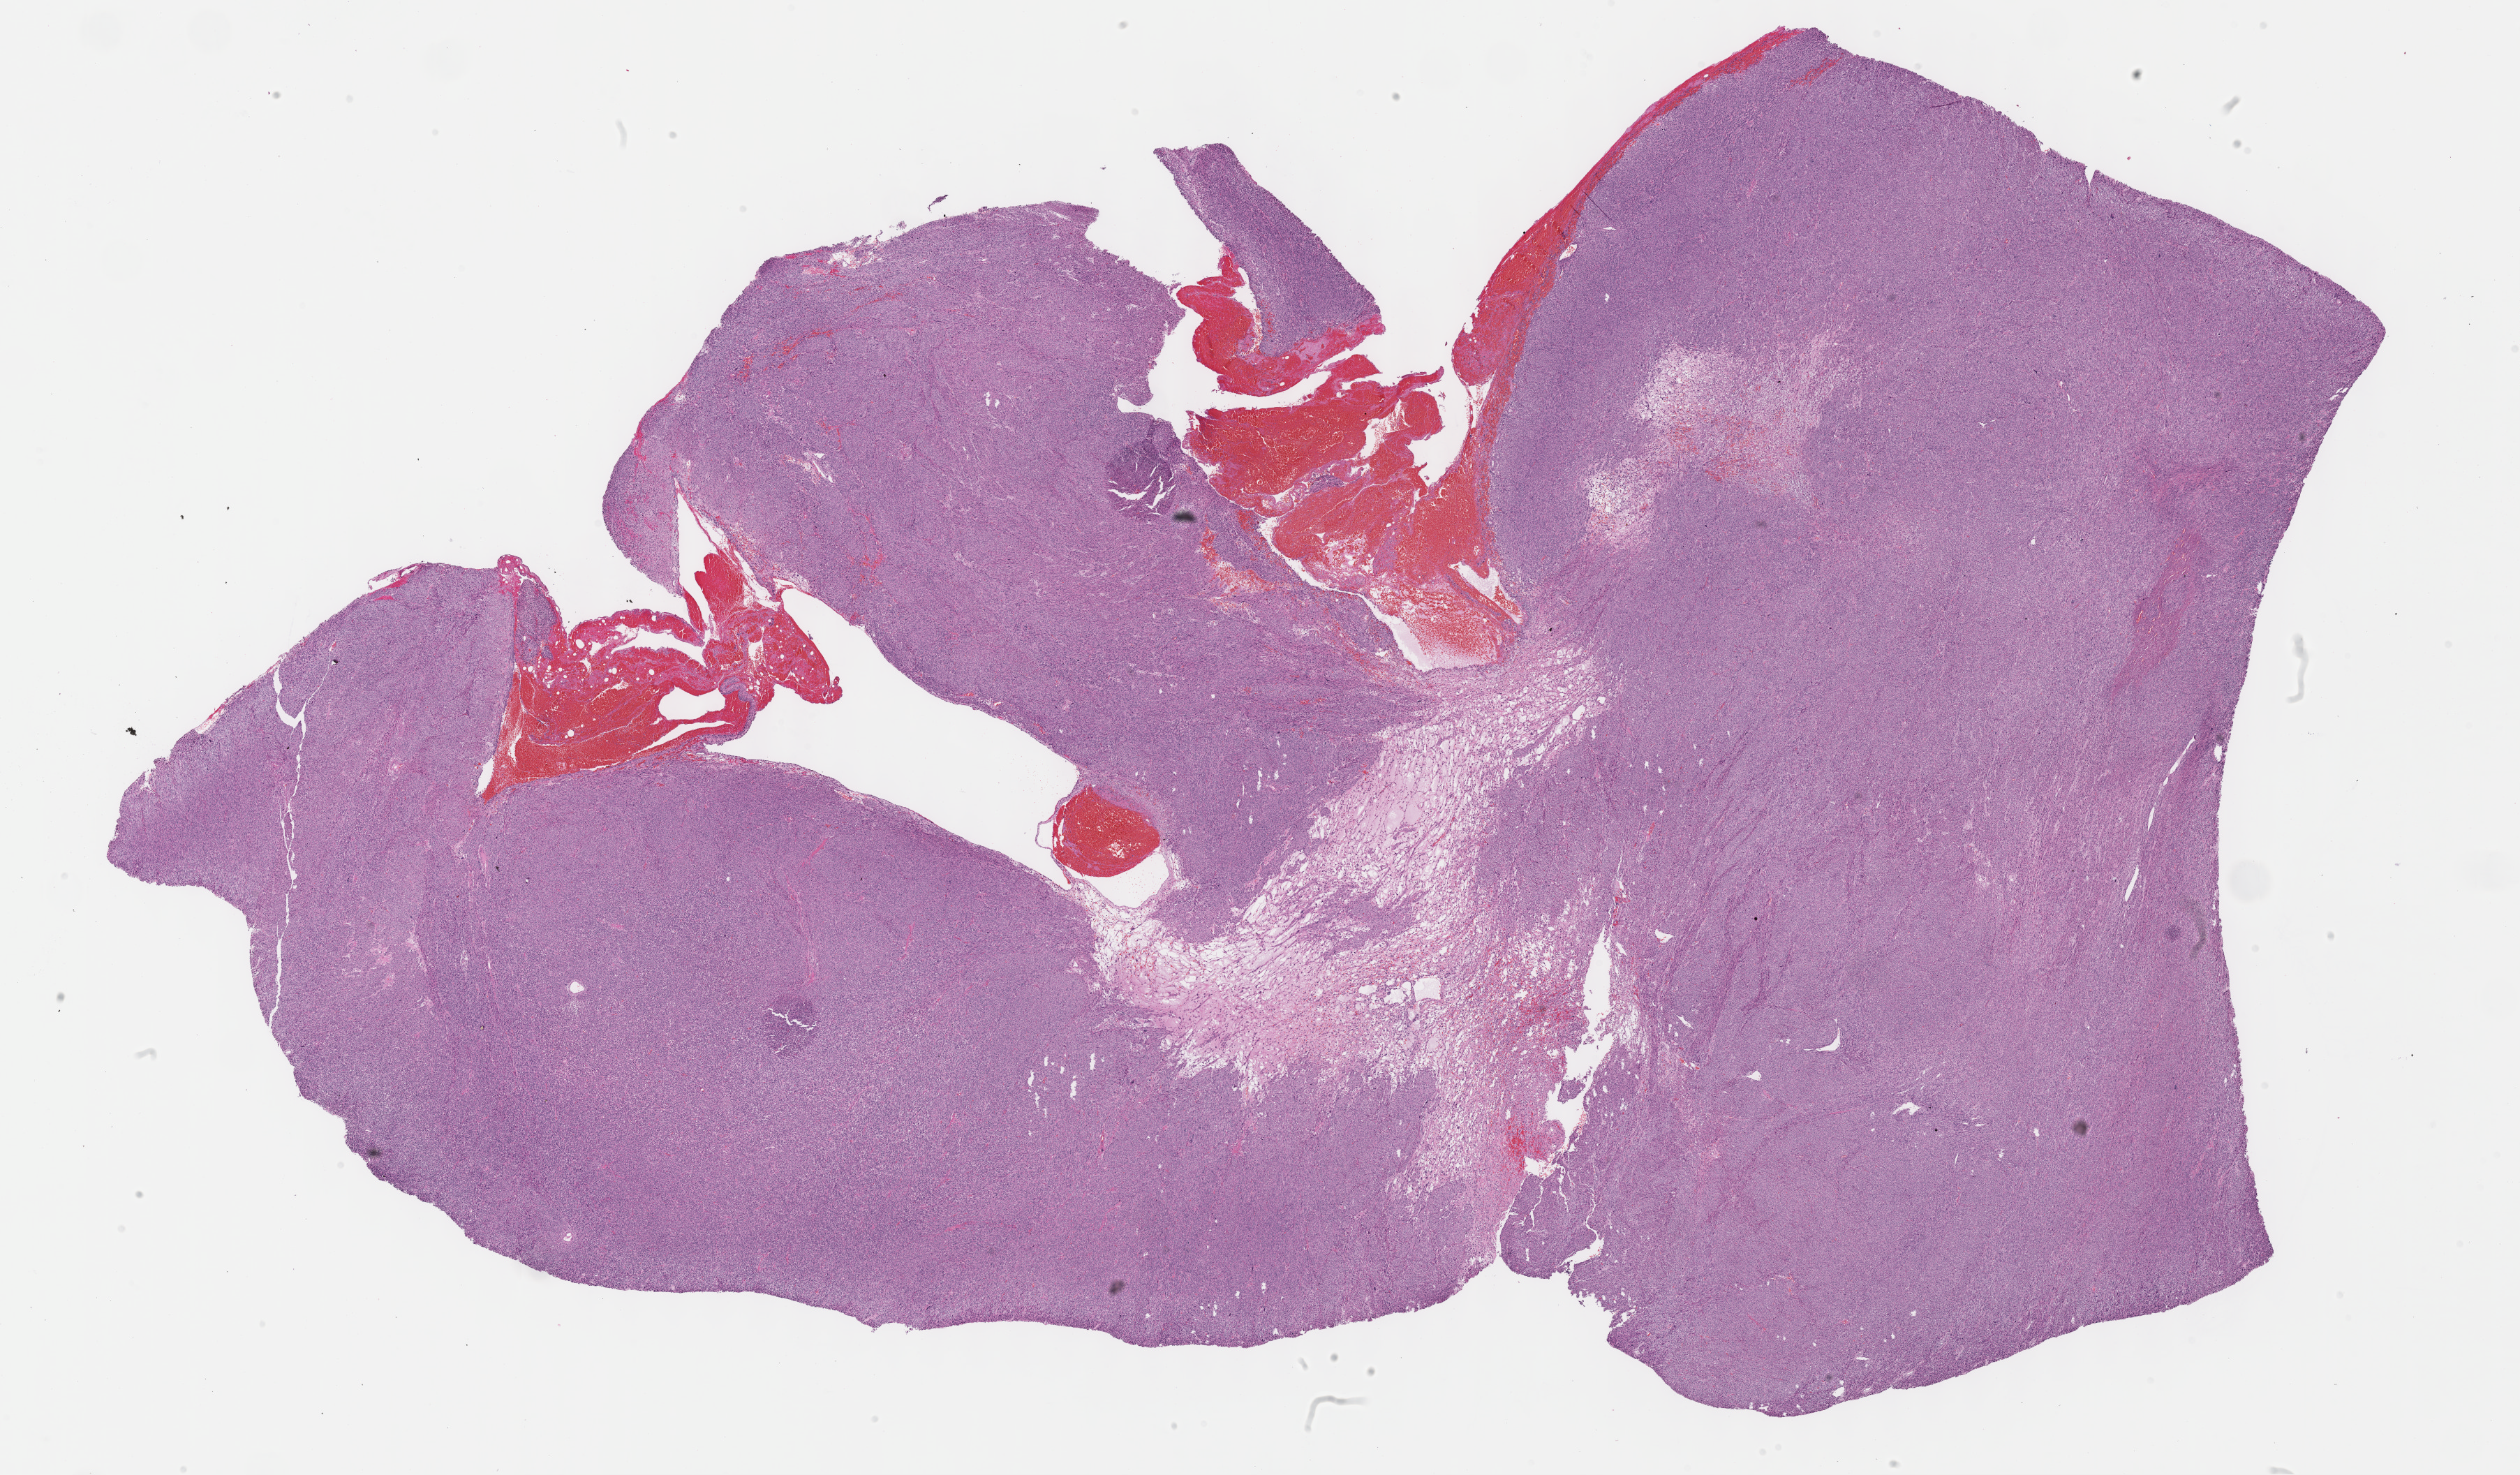
H&E whole-slide image — a low-resolution overview of the entire scanned area, about 29.2 x 17.1 mm (acquisition: 40x scan); formalin-fixed paraffin-embedded (FFPE) diagnostic section; sample: primary tumour, corpus uteri. Female, age 59 years at initial diagnosis.
Diagnosis: Leiomyosarcoma, NOS (myometrium).